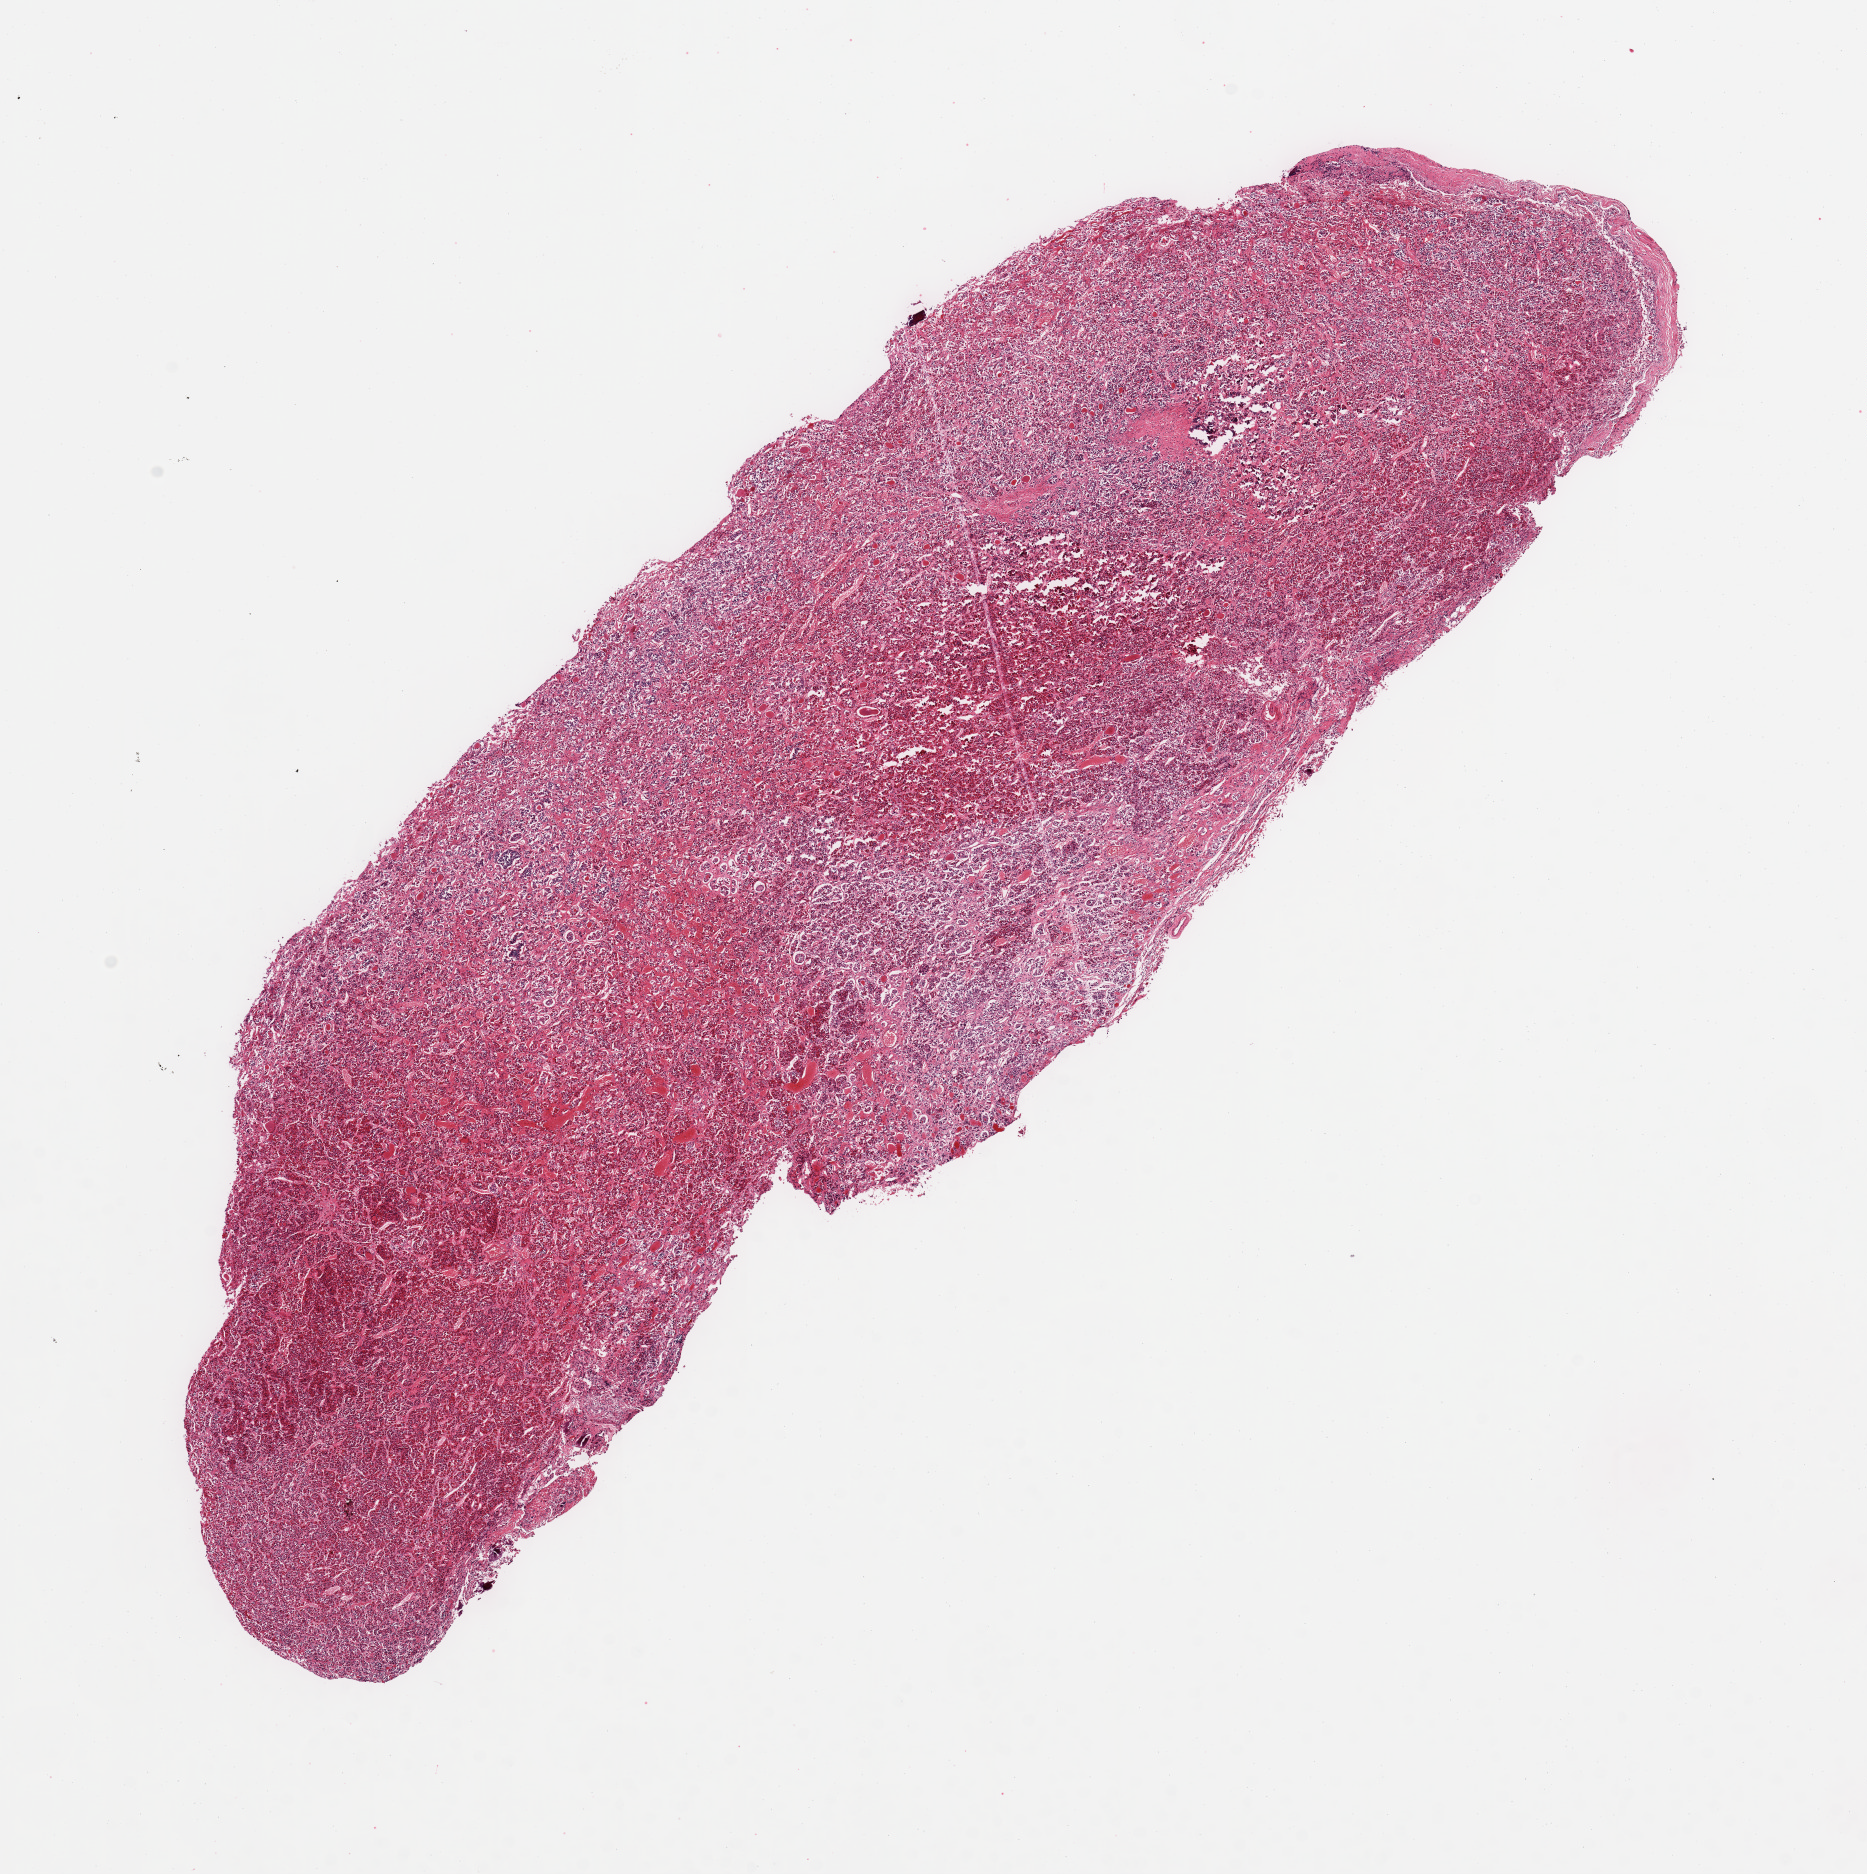
Digitized hematoxylin and eosin (H&E)-stained section, brightfield, shown as a low-resolution overview of the whole scanned area (about 14.8 x 14.8 mm). PAXgene-fixed, paraffin-embedded tissue. Section of pituitary (target tissue). Donor tissue sample.
Reviewer comment on this tissue sample: 1 piece; adenohypophysis in this section.